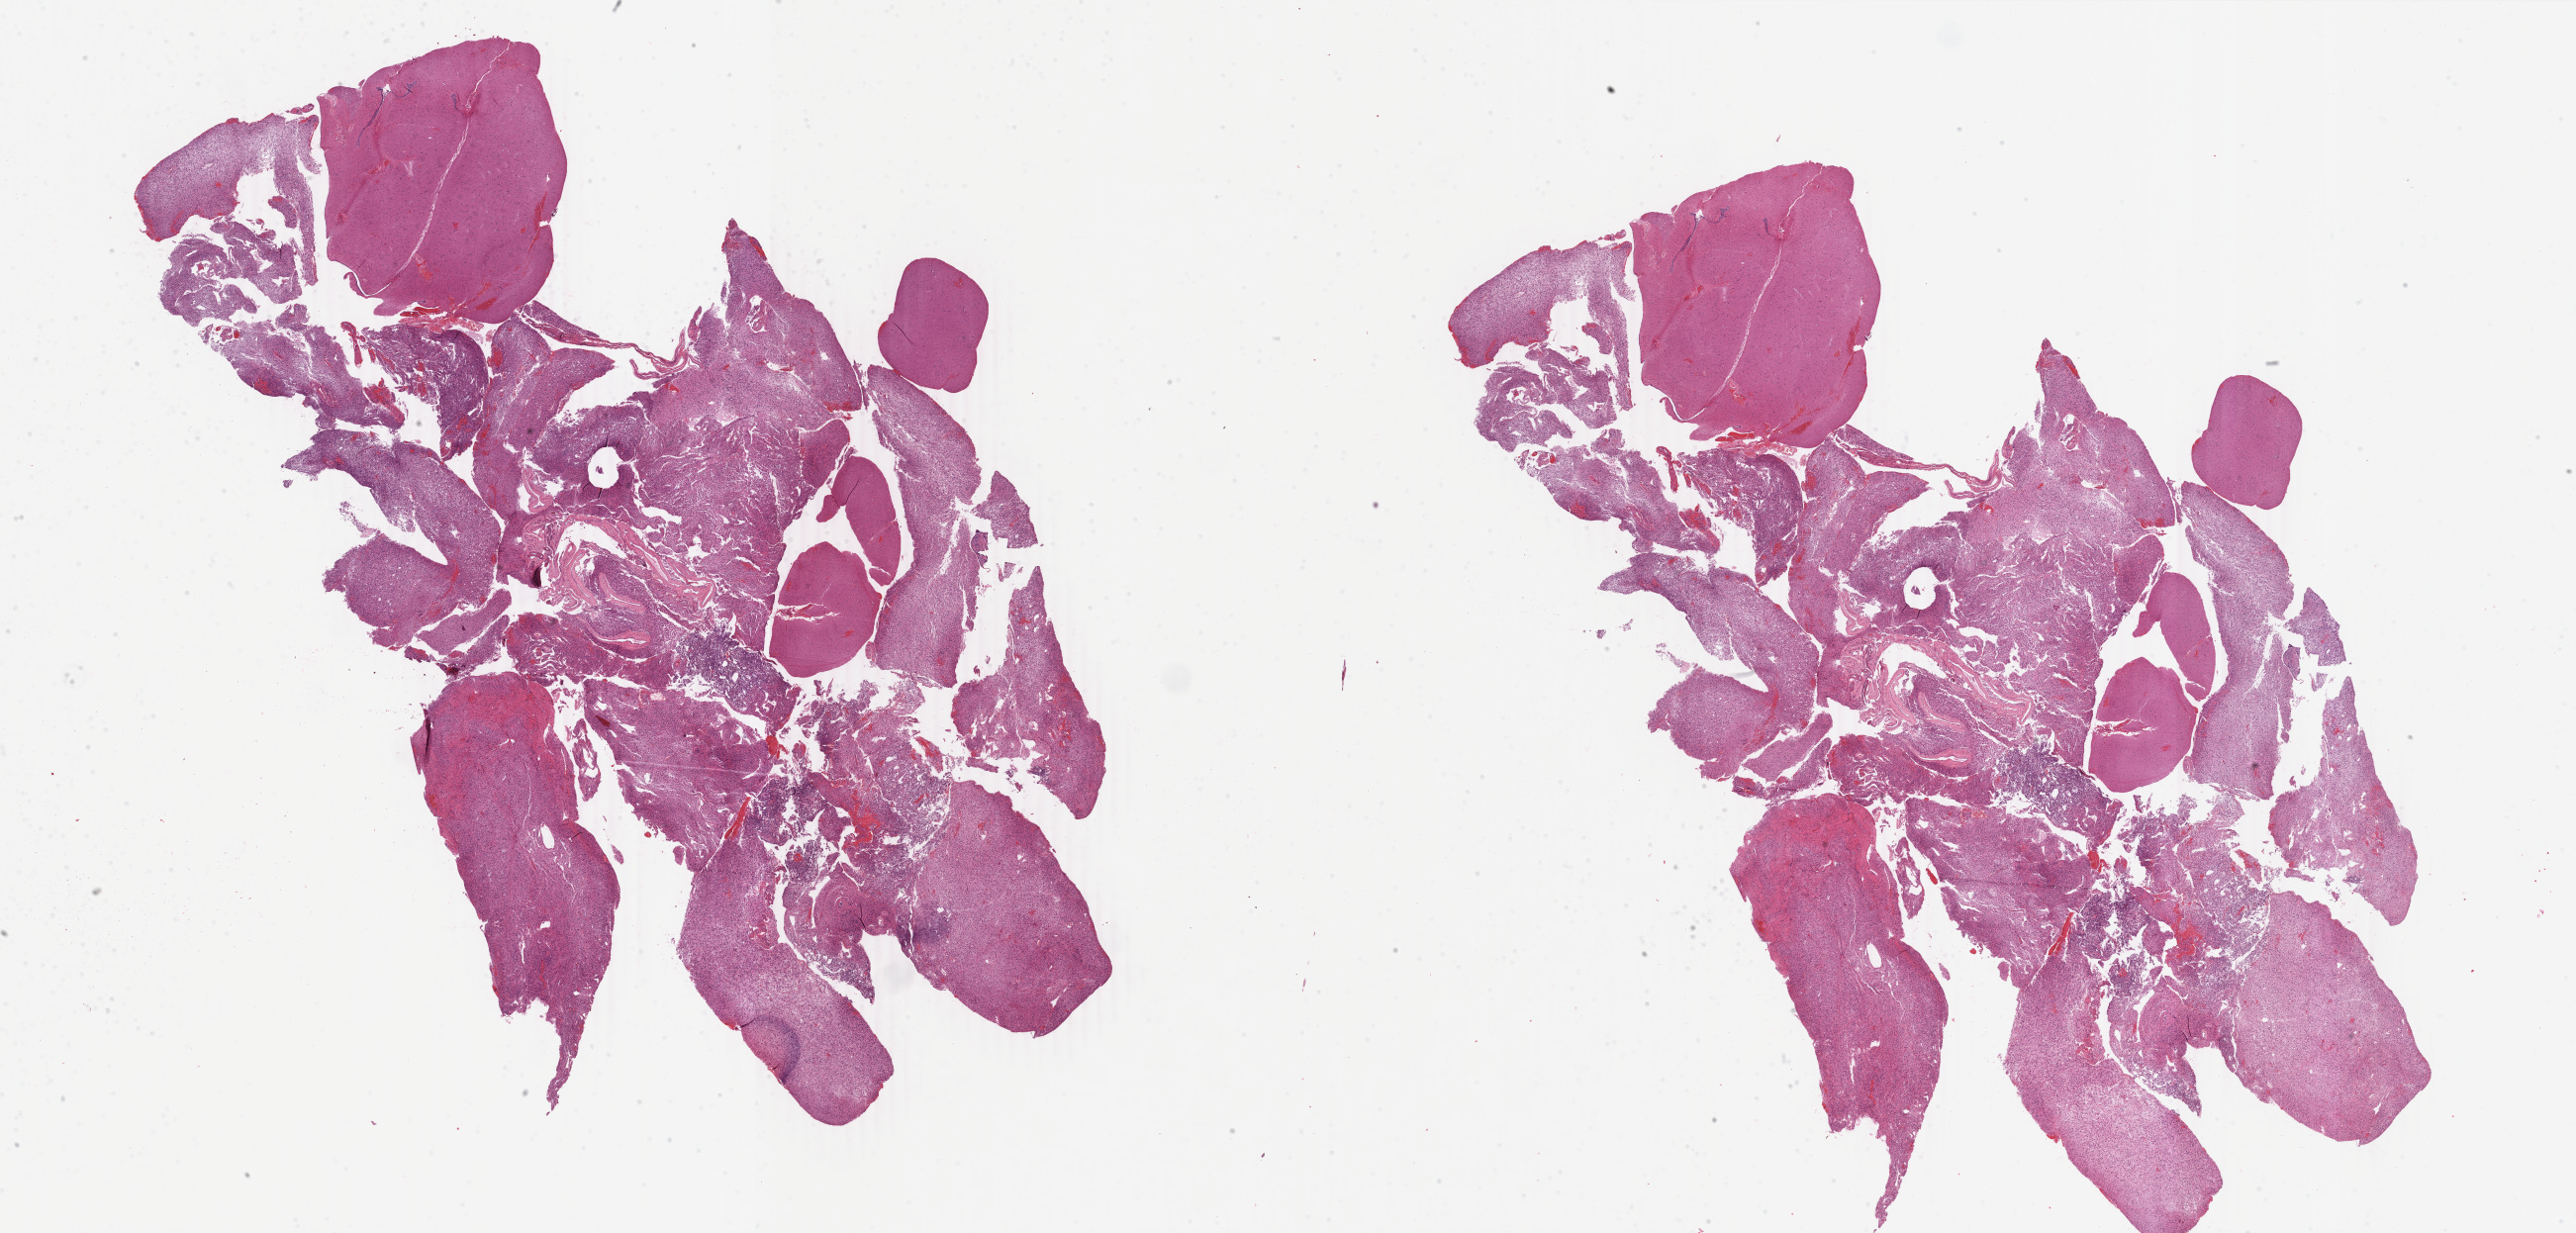
Hematoxylin and eosin (H&E) stained whole-slide image — shown as a low-resolution overview of the whole scanned area (about 41.4 x 19.8 mm, from a 40x scan). Formalin-fixed paraffin-embedded (FFPE) diagnostic section. Primary tumour sample from the brain. Male, age 49 years at initial diagnosis. Histologic grade: G3 (poorly differentiated).
Diagnosis: Astrocytoma, anaplastic (cerebrum).